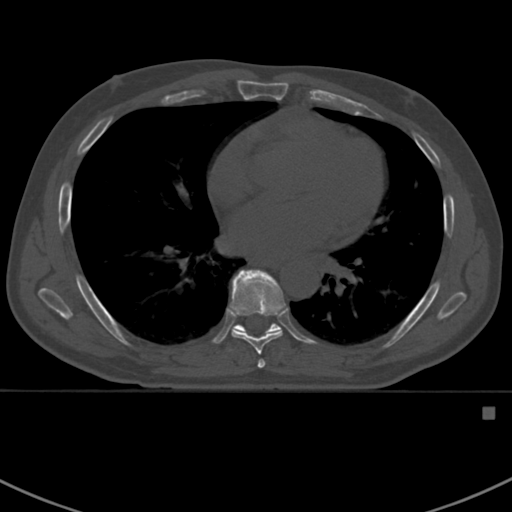
CT including the spine, one axial slice. Position 412 of 412 along the scan axis. Reconstruction kernel Br40s. 120 kVp. Bone window (W 1800 / L 400 HU). 512 × 512 image matrix. Patient: male, 59 years. Case-level facts recorded for this patient, not image findings: primary cancer: prostate.
Structures marked on this image (semi-automatic segmentation, software-assisted and operator-edited):
- T7 vertebra: bounding box (x1, y1, x2, y2) in pixels: (230, 269, 285, 368)
- T8 vertebra: (234, 273, 282, 335)